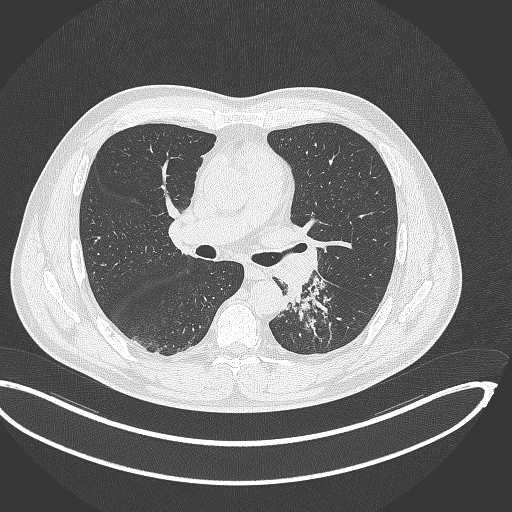
Chest CT, one axial slice; position 206 of 362 along the scan axis; reconstruction kernel B70f; lung window (W 1500 / L -600 HU); 1 mm slice thickness; 512 × 512 image matrix, field of view 442 × 442 mm. Patient: male, 50 years. From the clinical record (not read from this slice): clinical TNM (as recorded): T2a N3 M0.
Structures marked on this image (rectangle marked by the reading radiologist):
- lung tumour (recorded histology: squamous cell carcinoma): box from (x=284, y=282) to (x=304, y=306) px